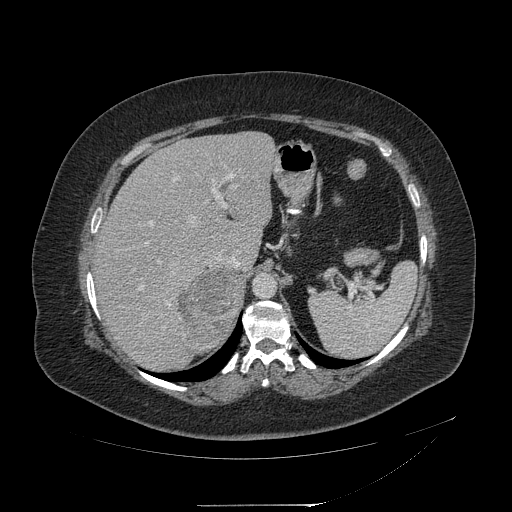
Contrast-enhanced abdominal CT, one axial slice. Slice 153 of 217 in the series (ordered by position). Intravenous contrast given. Soft-tissue window (W 400 / L 40 HU). 1.25 mm slice thickness. 512 × 512 image matrix. Female patient, age 55 years. Case-level facts recorded for this patient, not image findings: diagnosis: adrenocortical carcinoma; tumour side: right adrenal; tumour size at pathology: 11 cm; Ki-67 index: 20 %; stage (as recorded): 2.
Outlined on this slice (semi-automatic segmentation, software-assisted and operator-edited):
- mass: box from (x=180, y=269) to (x=242, y=352) px